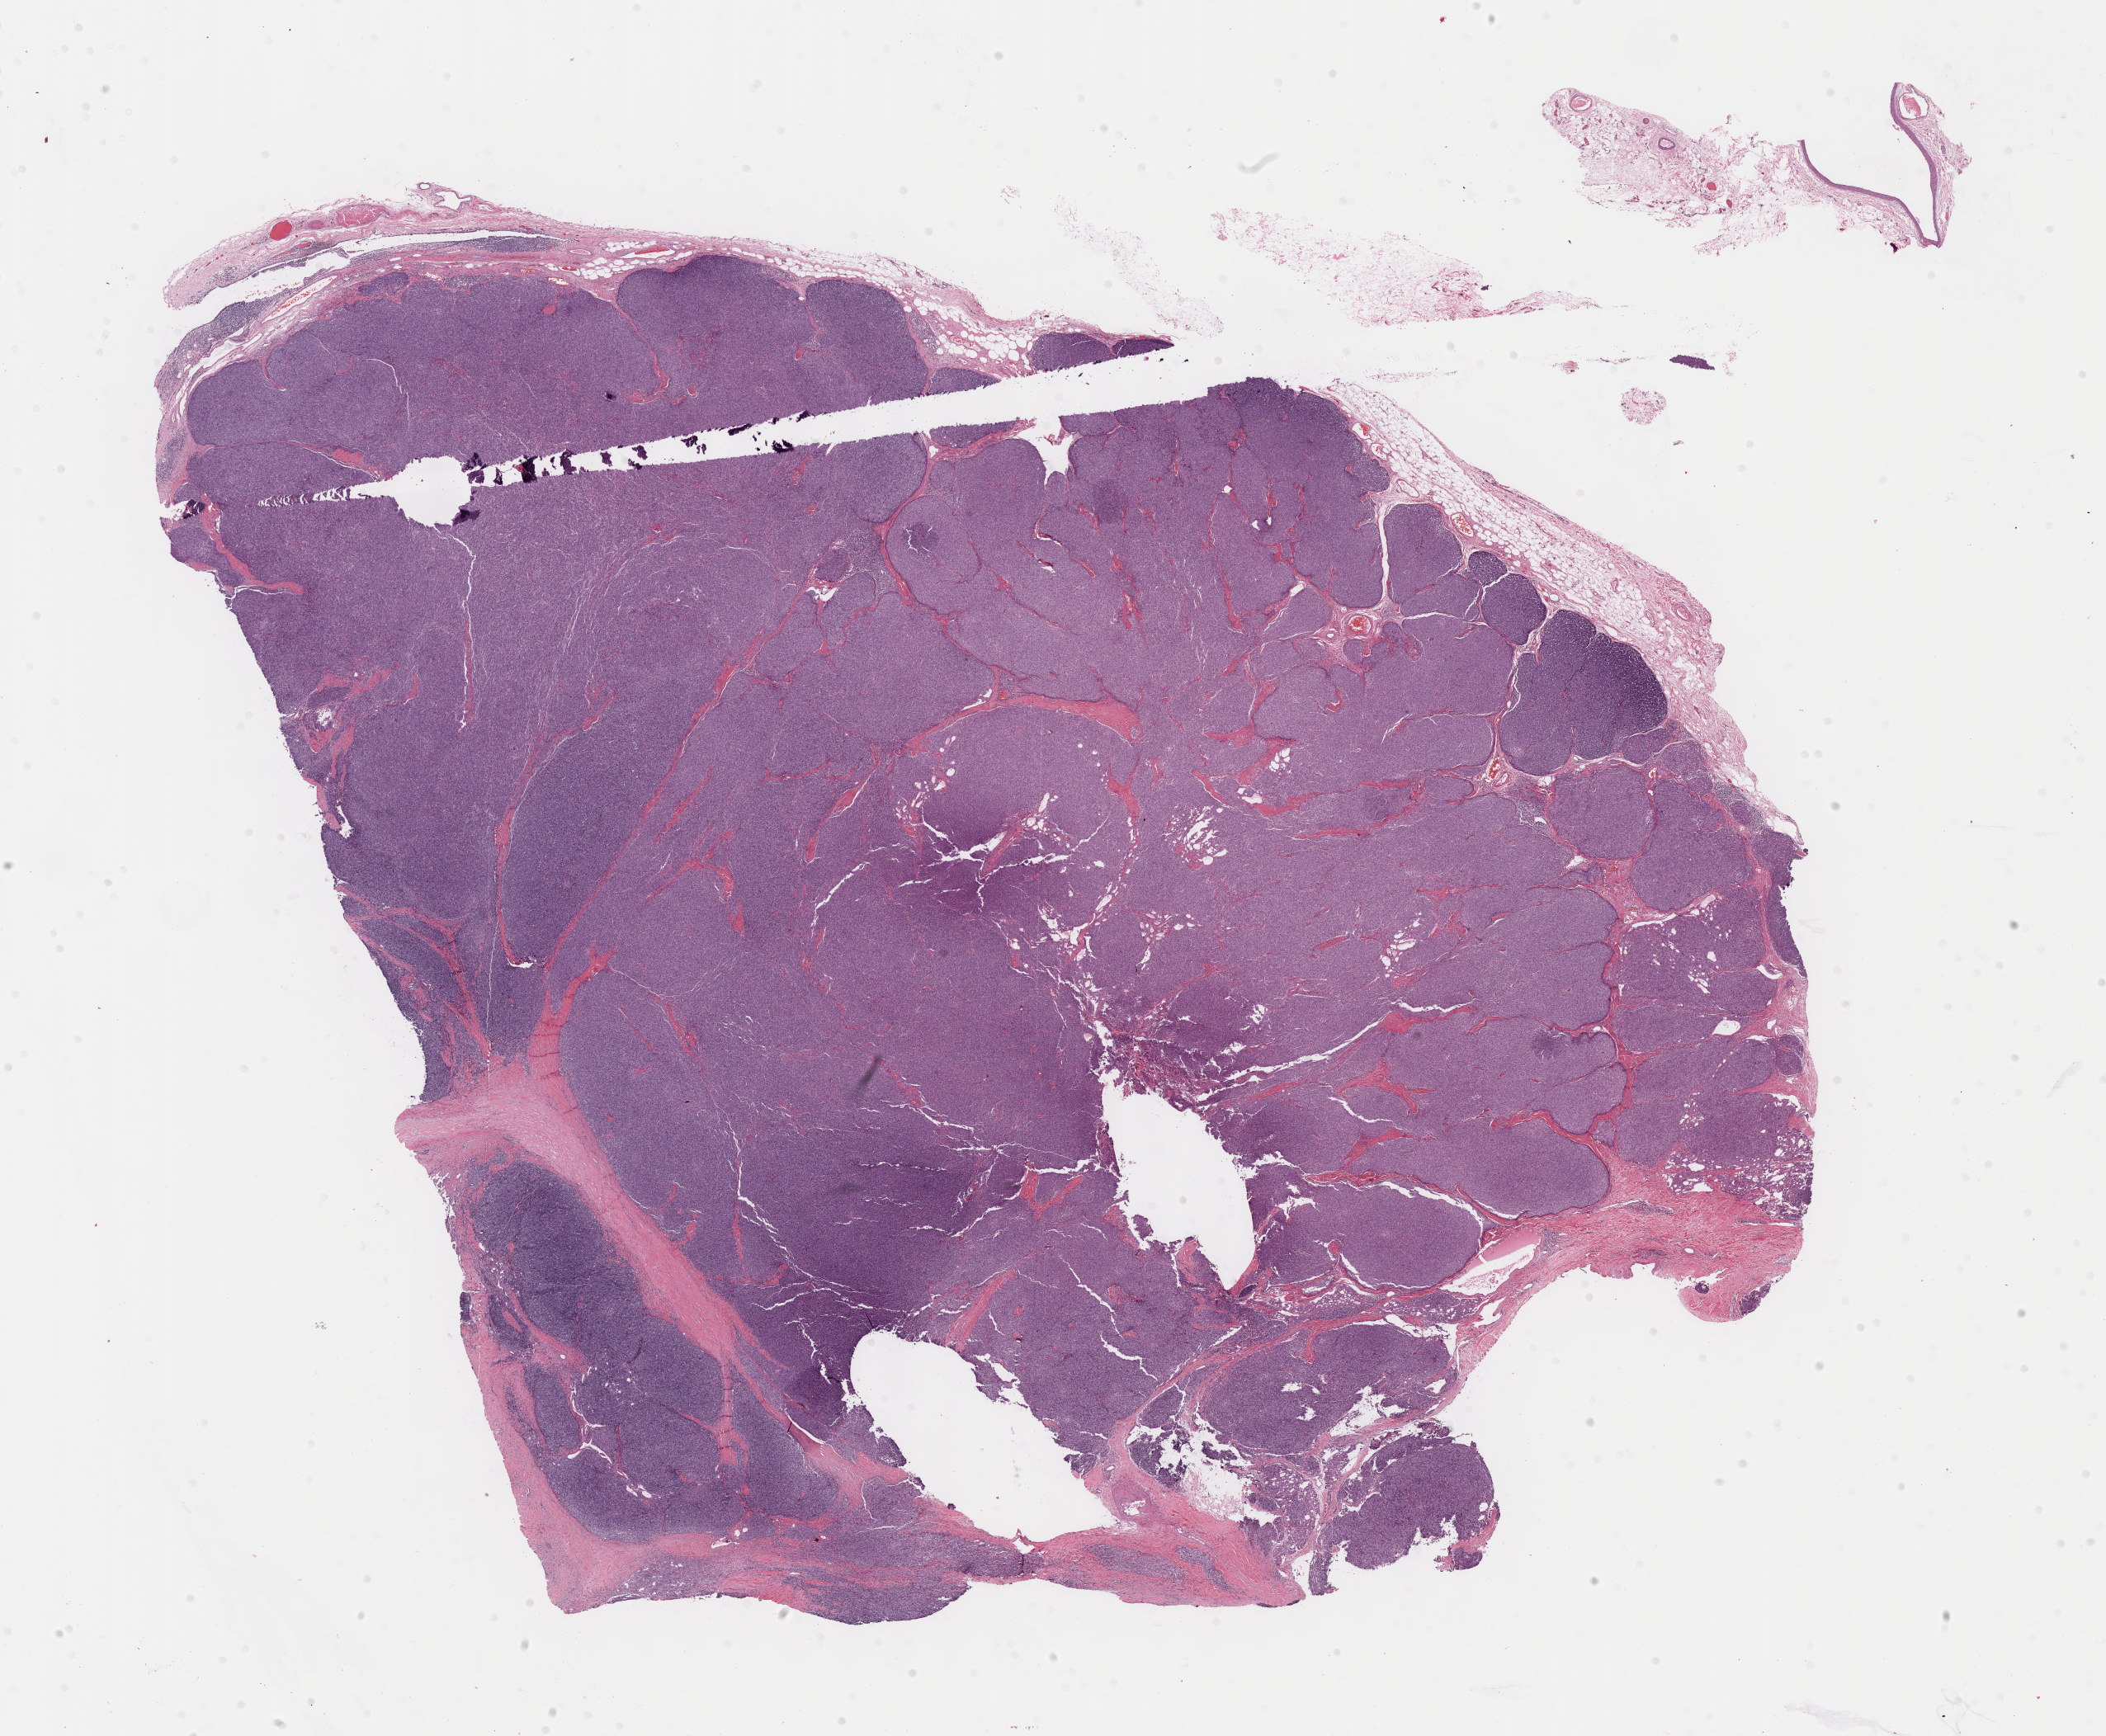
H&E-stained whole-slide image — shown as a low-resolution overview of the whole scanned area (about 20.6 x 17.0 mm). Formalin-fixed paraffin-embedded (FFPE) diagnostic section. Thymus, primary tumour sample. Male patient; age at initial diagnosis 54 years.
Histologic diagnosis: Thymoma, type A, malignant.